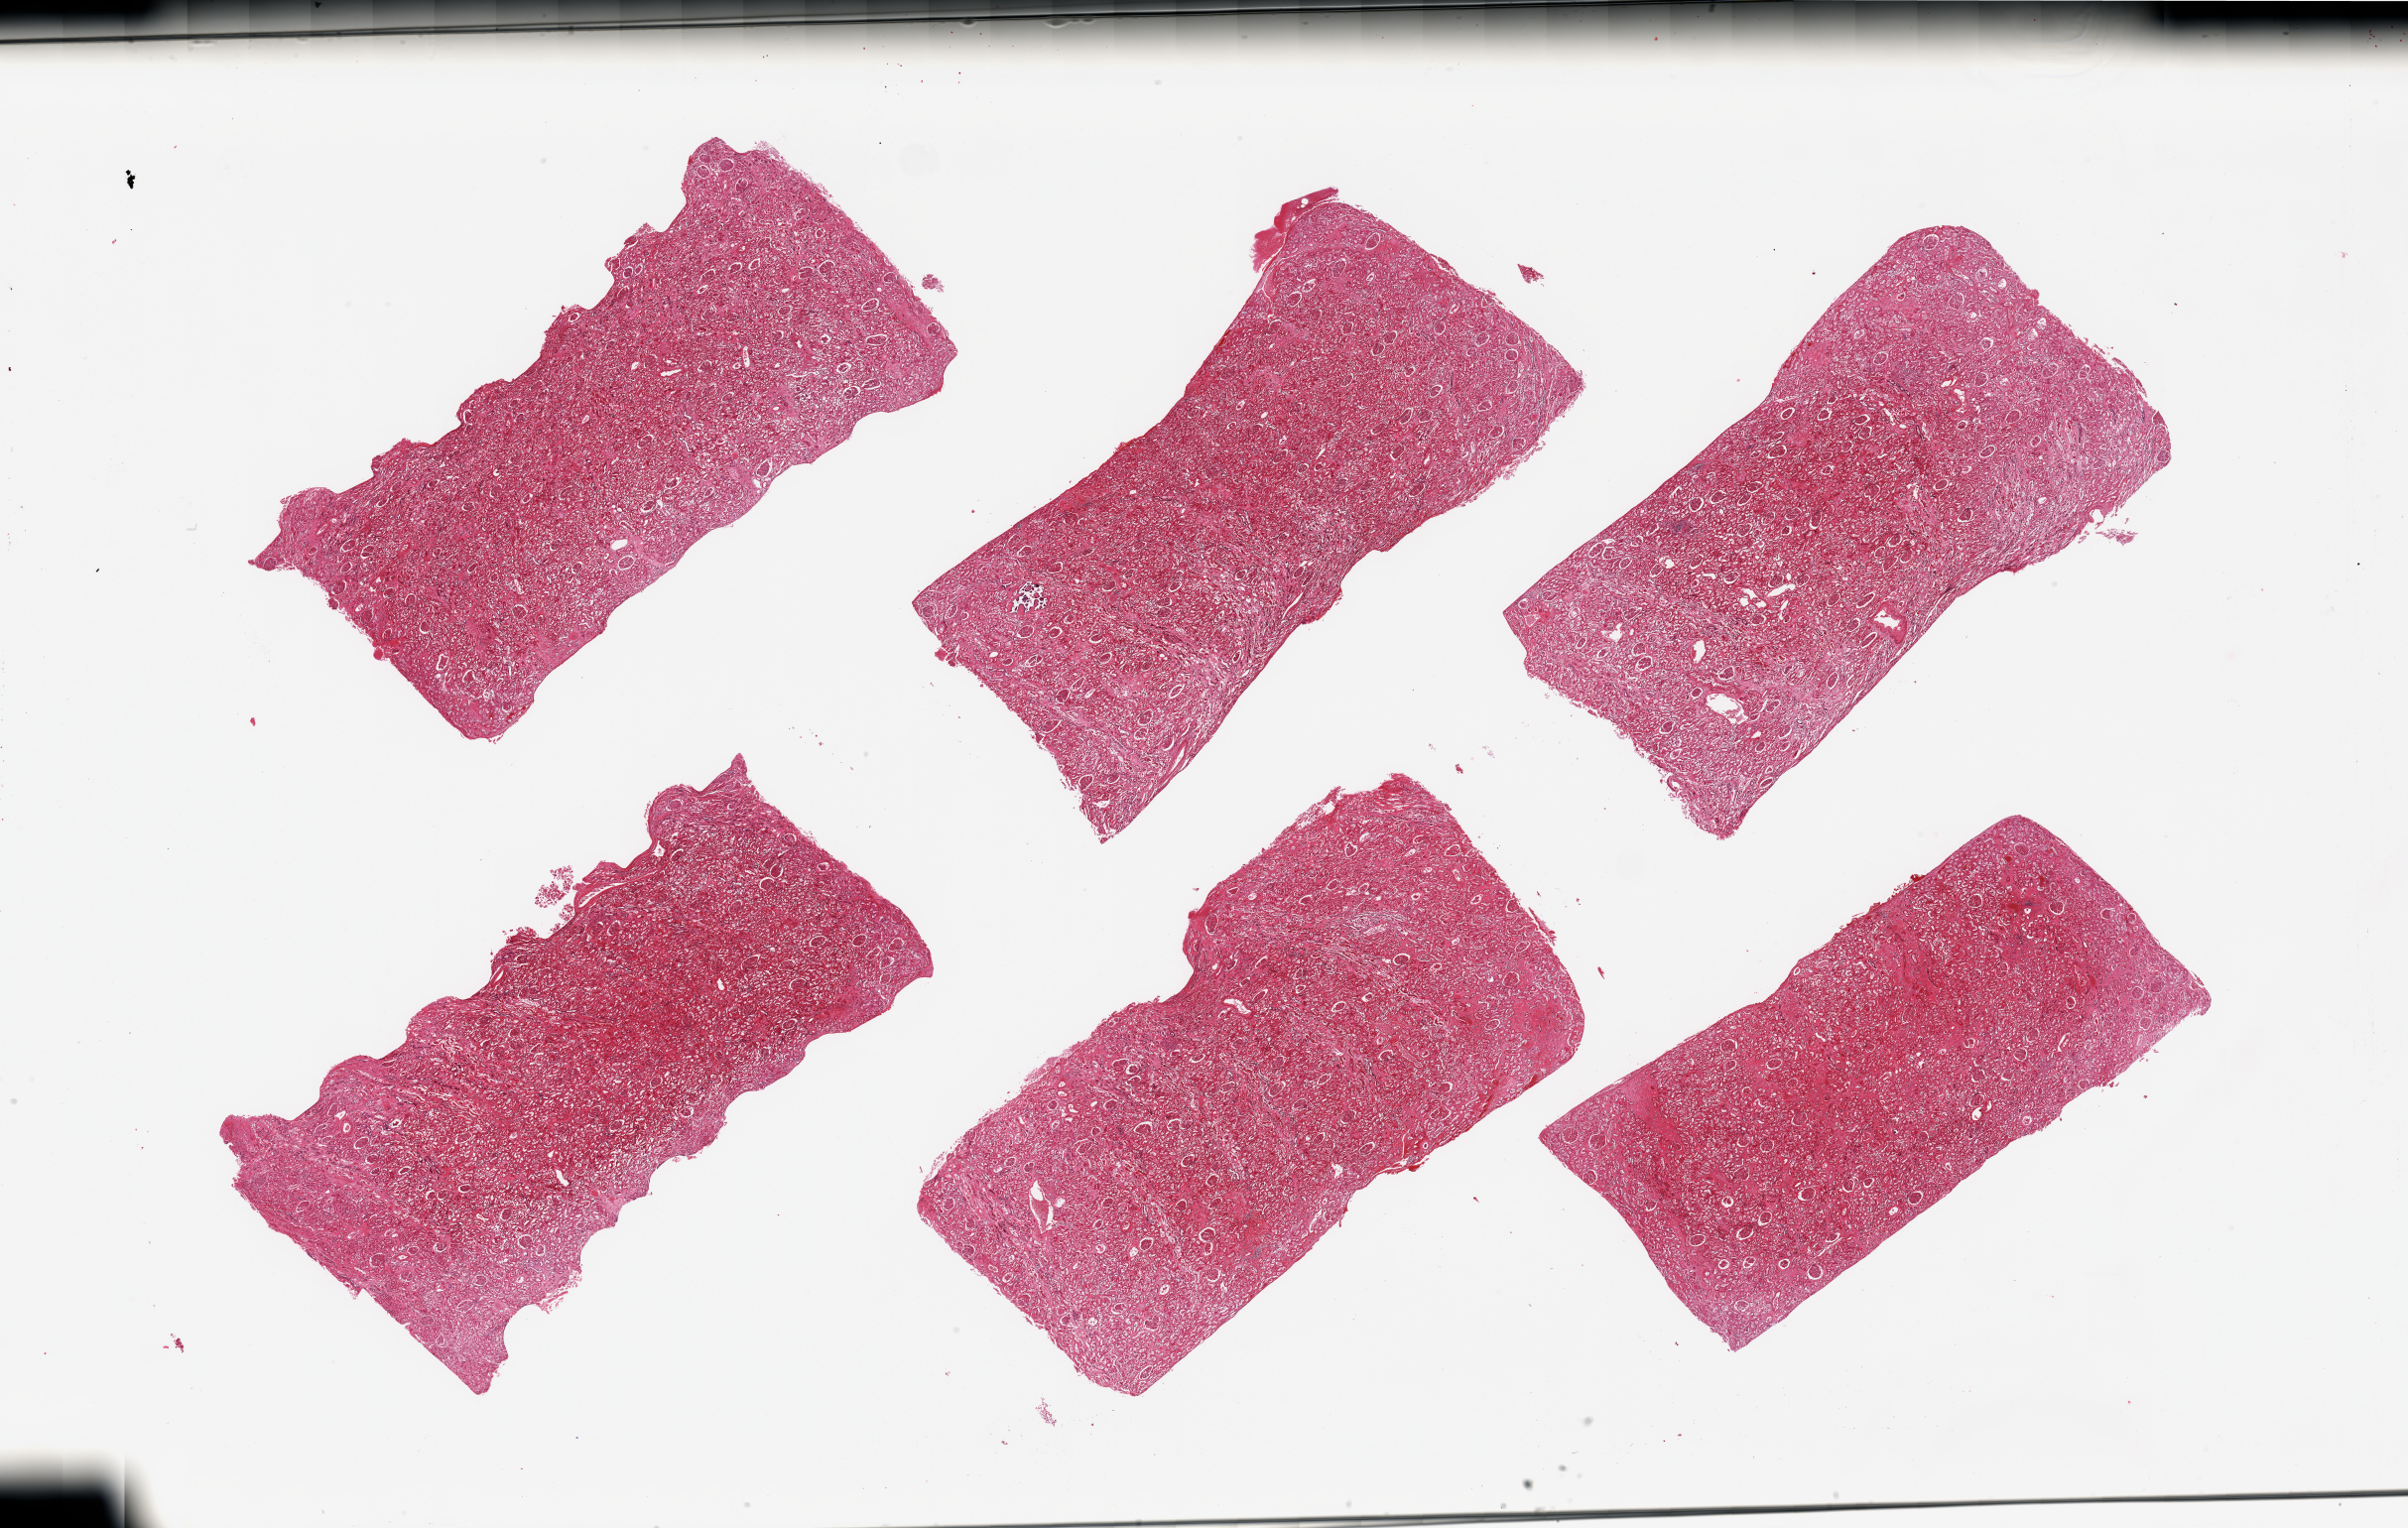
Digitized H&E-stained section, shown as a low-resolution overview of the whole scanned area (about 38.4 x 24.4 mm, slide scanned at 20x). PAXgene-fixed paraffin-embedded (PFPE) section. Section of renal cortex (target tissue). Tissue donor sample. Donor: male.
Pathologist's review note for this sample: 6 pieces; tubules severely autolyzed; glomeruli somewhat less; scattered interstitial and glomerular scars.